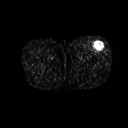
FDG PET of an extremity soft-tissue mass (from a PET/CT study), one axial slice; position 223 of 267 along the scan axis; 3.27 mm slice thickness; 128 × 128 image matrix, field of view 500 × 500 mm. Patient: male, 64 years. Case-level facts recorded for this patient, not image findings: histological type: extraskeletal osteosarcoma; grade: high; site of the primary tumour: thigh.
Annotated regions visible in this slice (expert contour drawn on MRI and transferred to this co-registered scan by the dataset authors):
- gross tumour volume (mass): bounding box [x1, y1, x2, y2] px = [93, 42, 104, 51]